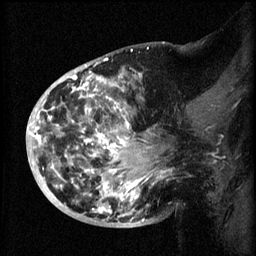
Breast MRI (dynamic contrast-enhanced), one sagittal slice. Position 26 of 60 along the scan axis. 3 images stored at this slice position (order not interpretable as contrast timing). 1.5 T. TE 4.2 ms, TR 8.2 ms. 2 mm slice thickness. 256 × 256 image matrix, field of view 200 × 200 mm. Patient: female, 50 years.
Annotated regions visible in this slice (semi-automatically segmented with operator editing):
- analysis volume of interest (the breast-tissue region the enhancement analysis was run in; not a lesion): bounding box [x1, y1, x2, y2] px = [44, 72, 172, 219]
- tumour enhancement mask (voxels above the 70 % enhancement threshold inside the analysis volume of interest): [45, 72, 167, 217]